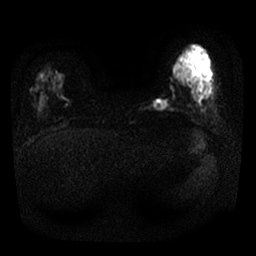
Breast MRI, one axial slice; diffusion-weighted series; image 2 of 4 stored at this slice position (different b-values; order by instance number); 1.5 T; 4 mm slice thickness; 256 × 256 image matrix, field of view 300 × 300 mm. Female patient.
Outlined on this slice (manually delineated by an expert):
- tumour on diffusion-weighted imaging: box from (x=154, y=100) to (x=167, y=109) px